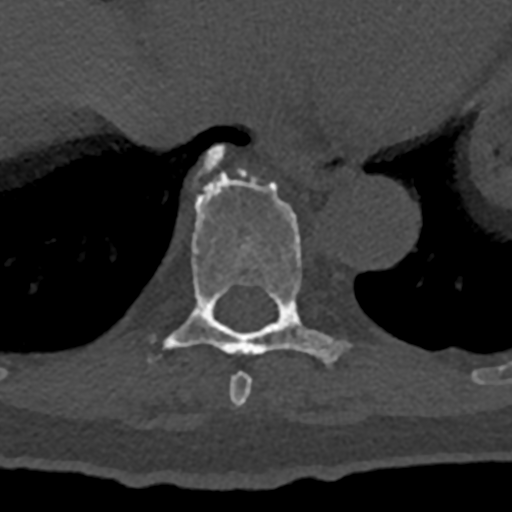
CT including the spine, one axial slice; position 658 of 797 along the scan axis; reconstruction kernel Br40s/3; bone window (W 1800 / L 400 HU); 0.5 mm slice thickness; 512 × 512 image matrix. Patient: male, 74 years. From the clinical record (not read from this slice): primary cancer: renal.
Outlined on this slice (semi-automatic segmentation, software-assisted and operator-edited):
- T8 vertebra: bounding box <229,373,252,411> (left, top, right, bottom; pixels)
- T9 vertebra: <166,146,348,358>